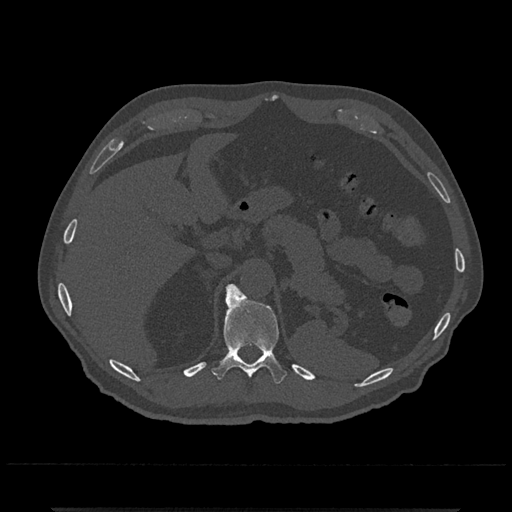
CT including the spine, one axial slice; position 492 of 797 along the scan axis; 120 kVp; bone window (W 1800 / L 400 HU); 0.5 mm slice thickness; 512 × 512 image matrix, field of view 393 × 393 mm. Patient: male, 67 years. From the clinical record (not read from this slice): primary cancer: prostate.
Annotated regions visible in this slice (semi-automatically segmented with operator editing):
- T11 vertebra: box from (x=212, y=284) to (x=287, y=384) px